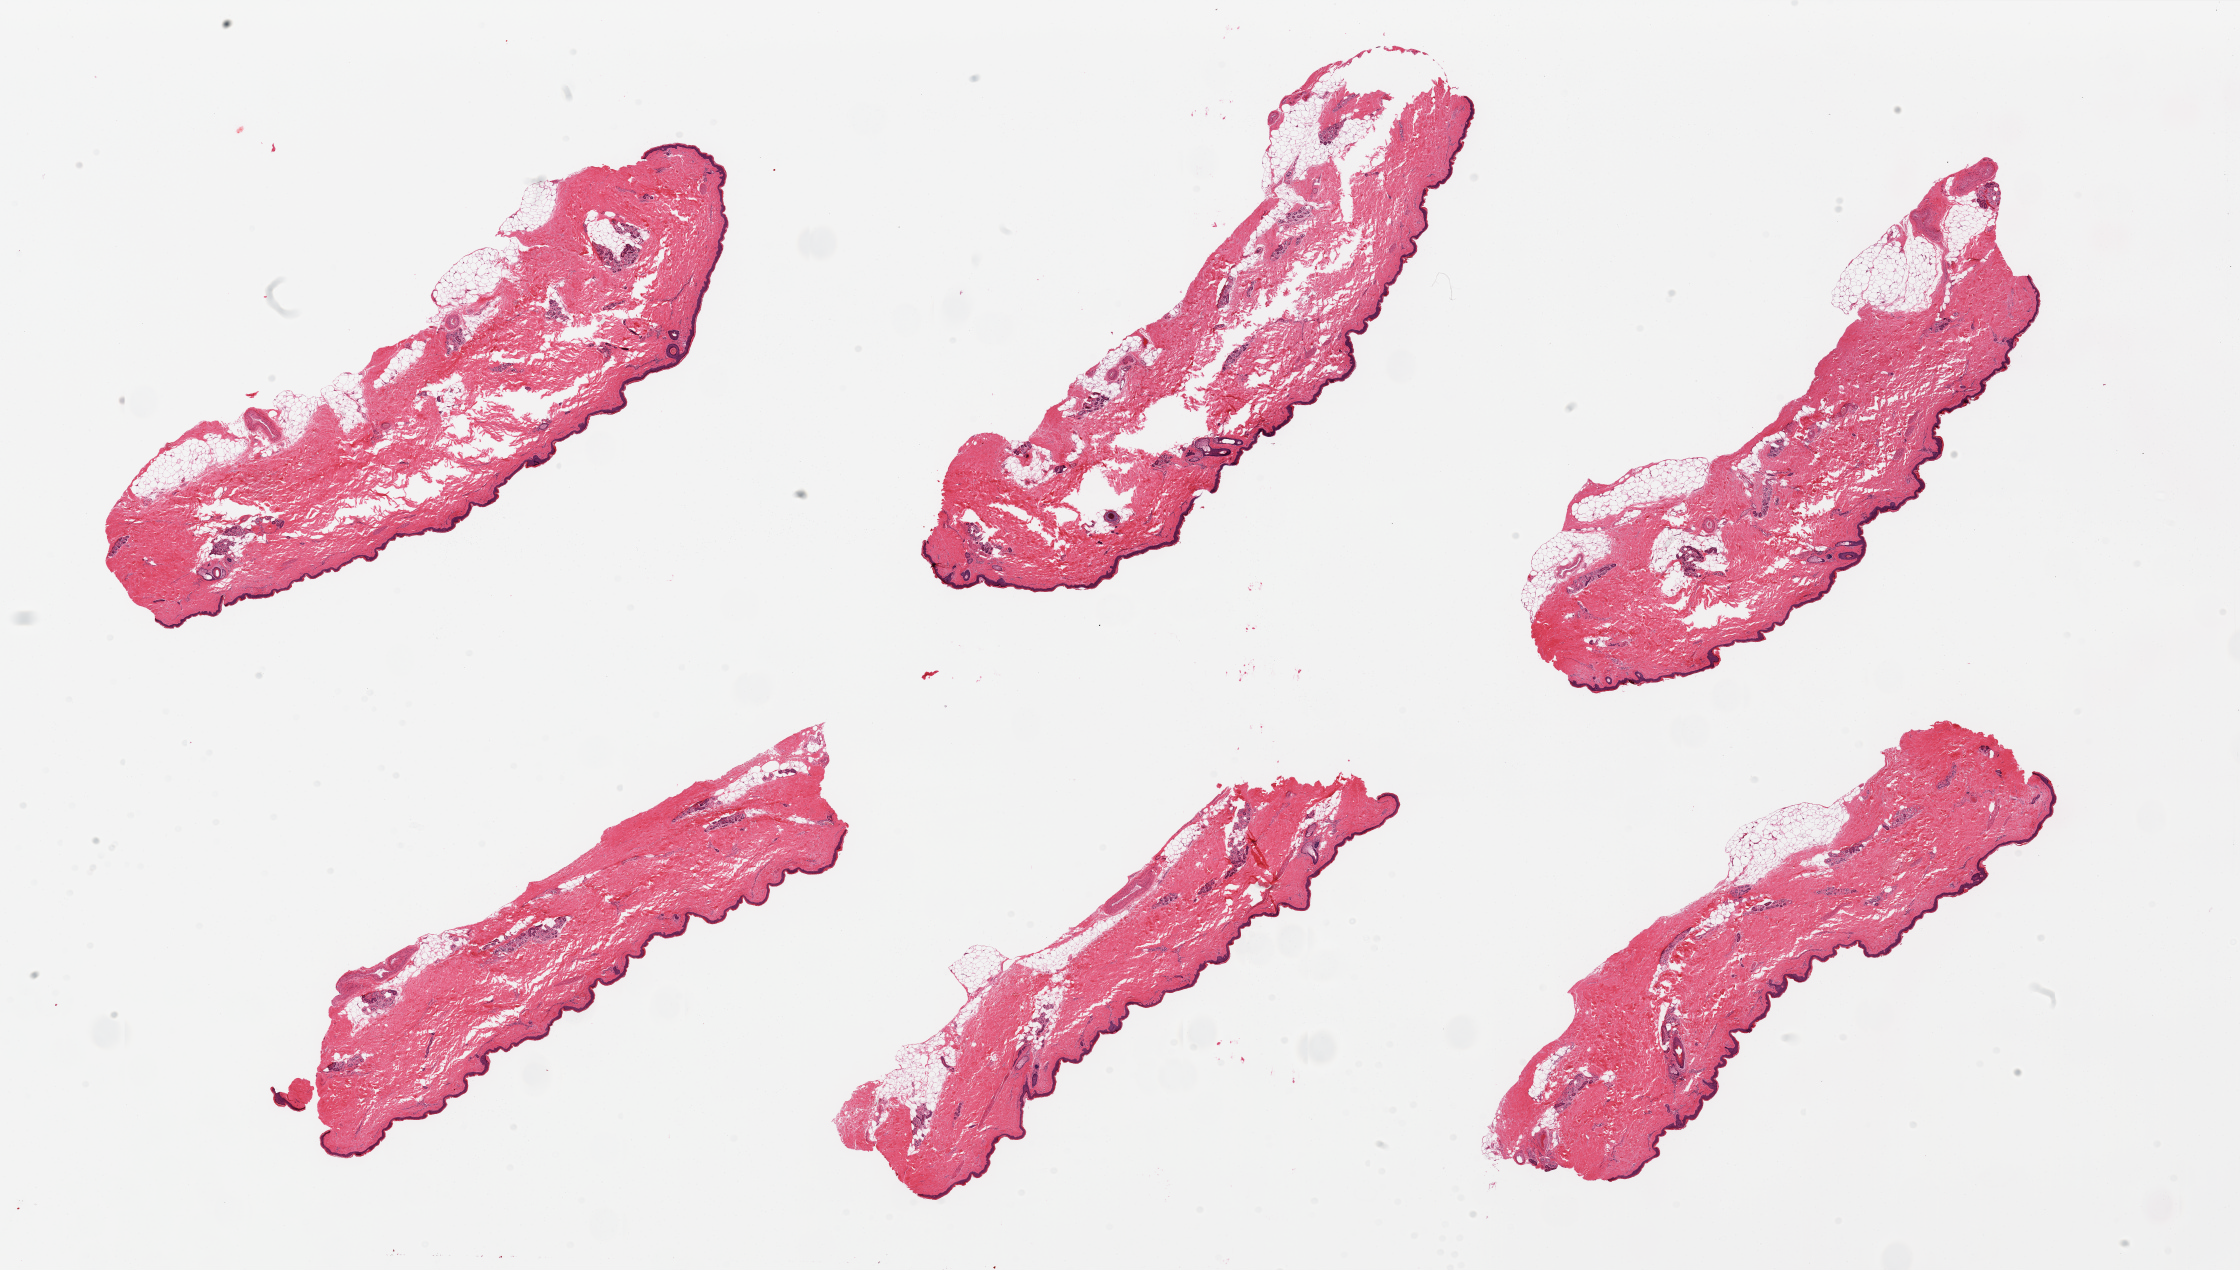
Digitized H&E-stained section — low-resolution overview of the scanned area, about 35.4 x 20.1 mm (slide scanned at 20x). PAXgene-fixed, paraffin-embedded tissue. Target tissue: skin of lower leg. Tissue donor sample.
• review note (as recorded): 6 pieces trace dermal fat, squamous epithelium is ~70-80 microns